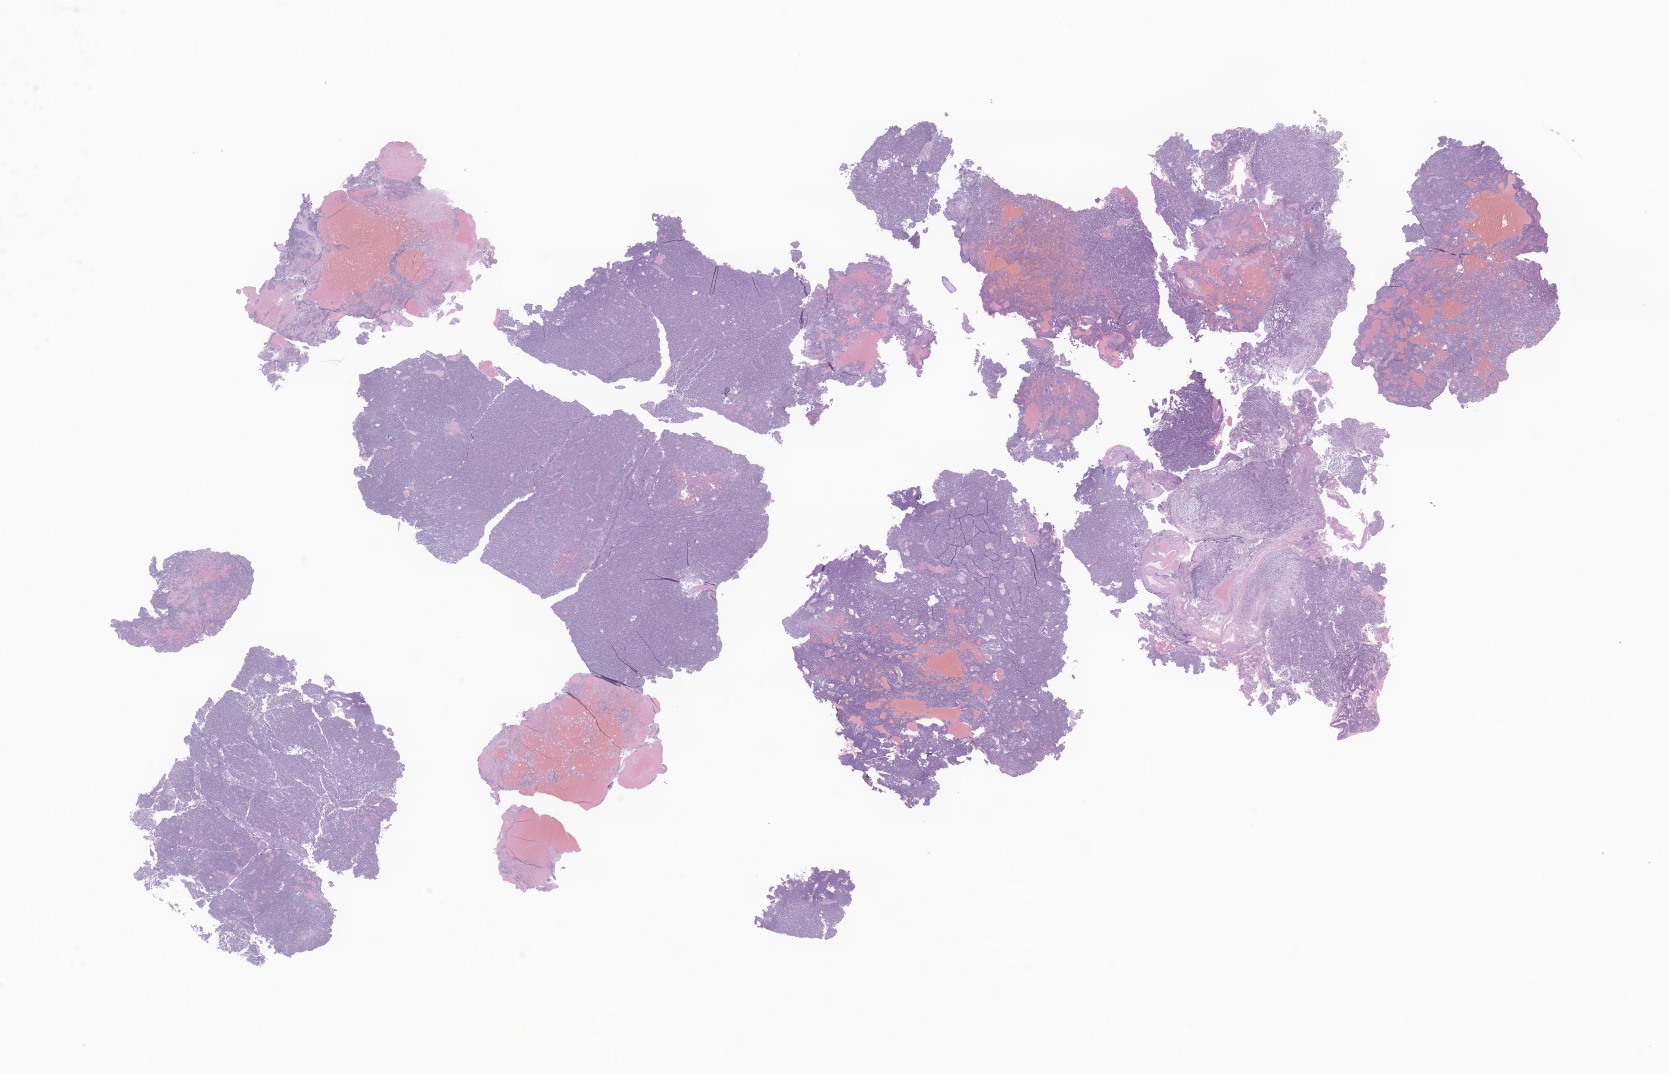
Haematoxylin and eosin whole-slide image of tumor tissue from the cerebral ventricle — whole scanned area (about 28.2 x 18.1 mm) shown as a low-resolution overview. FFPE section. Patient female; age 92 months (7 years 8 months).
• diagnosis: Medulloblastoma, NOS